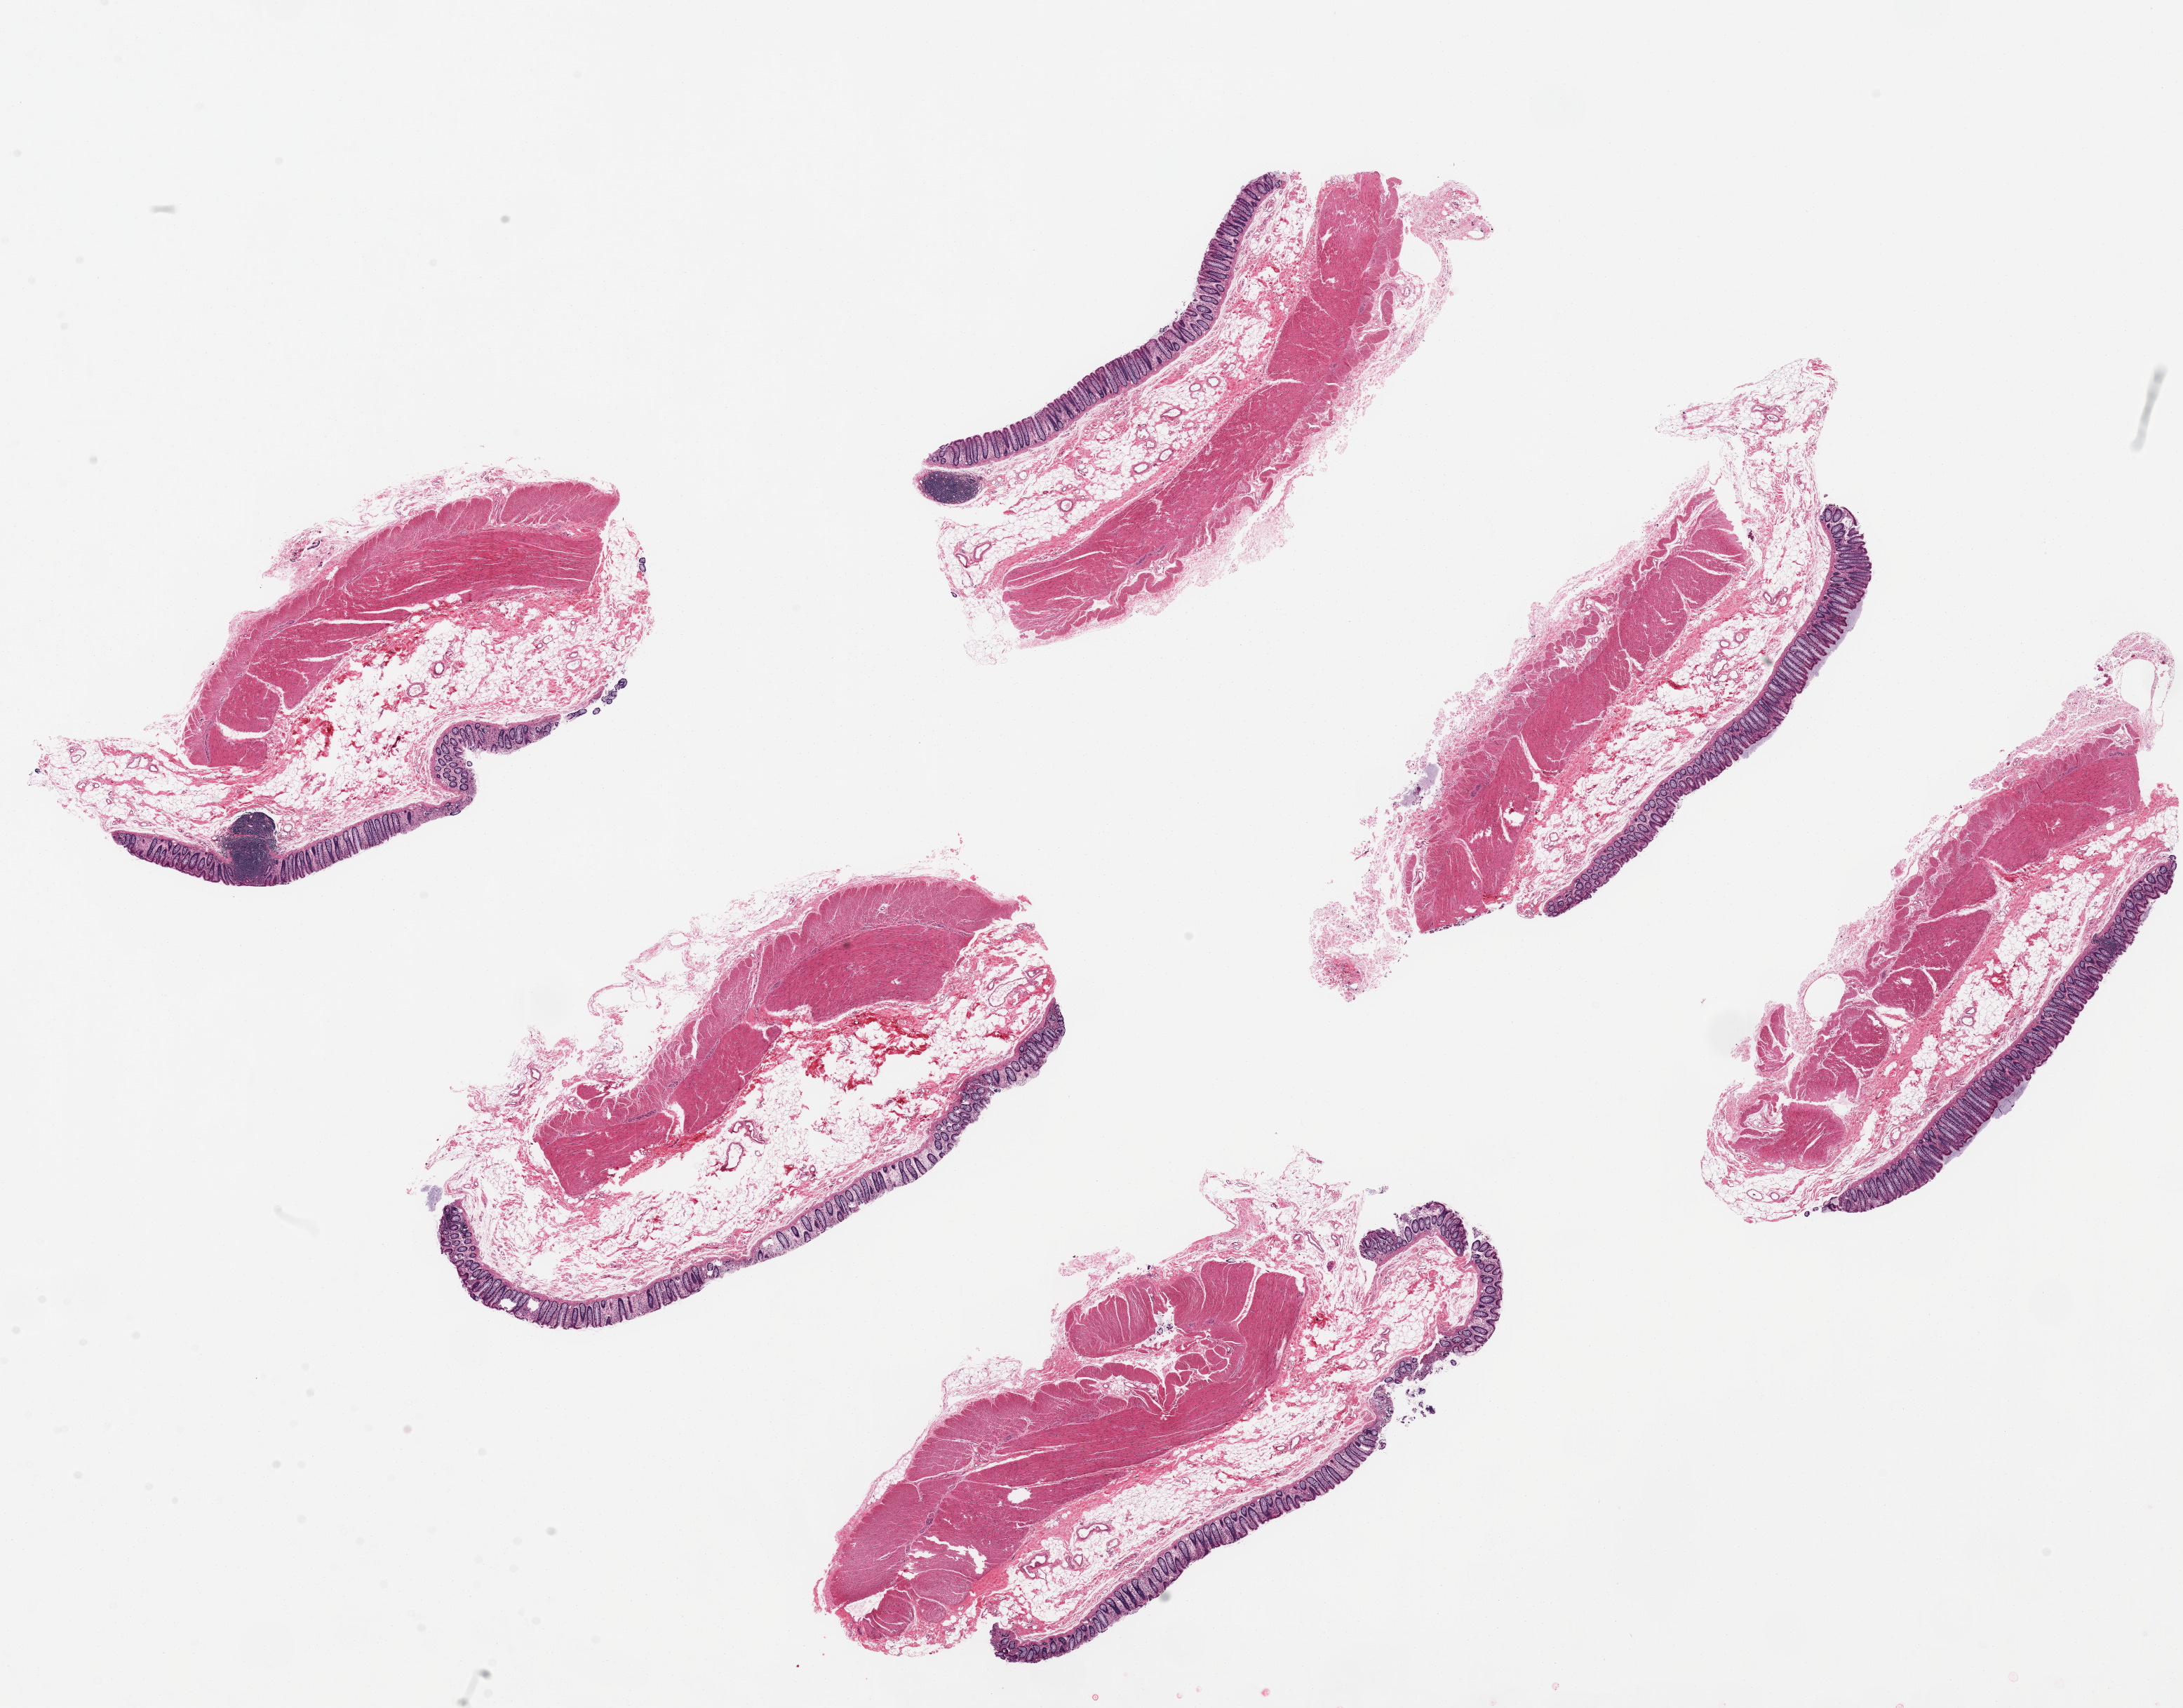
H&E whole-slide image, a low-resolution overview of the entire scanned area, about 24.6 x 19.3 mm, PAXgene-fixed, paraffin-embedded tissue, target tissue: transverse colon, tissue donor sample. Female donor.
• pathologist's review note for this sample: 6 pieces up to ~8x3 mm; mucosa up to 0.4mm